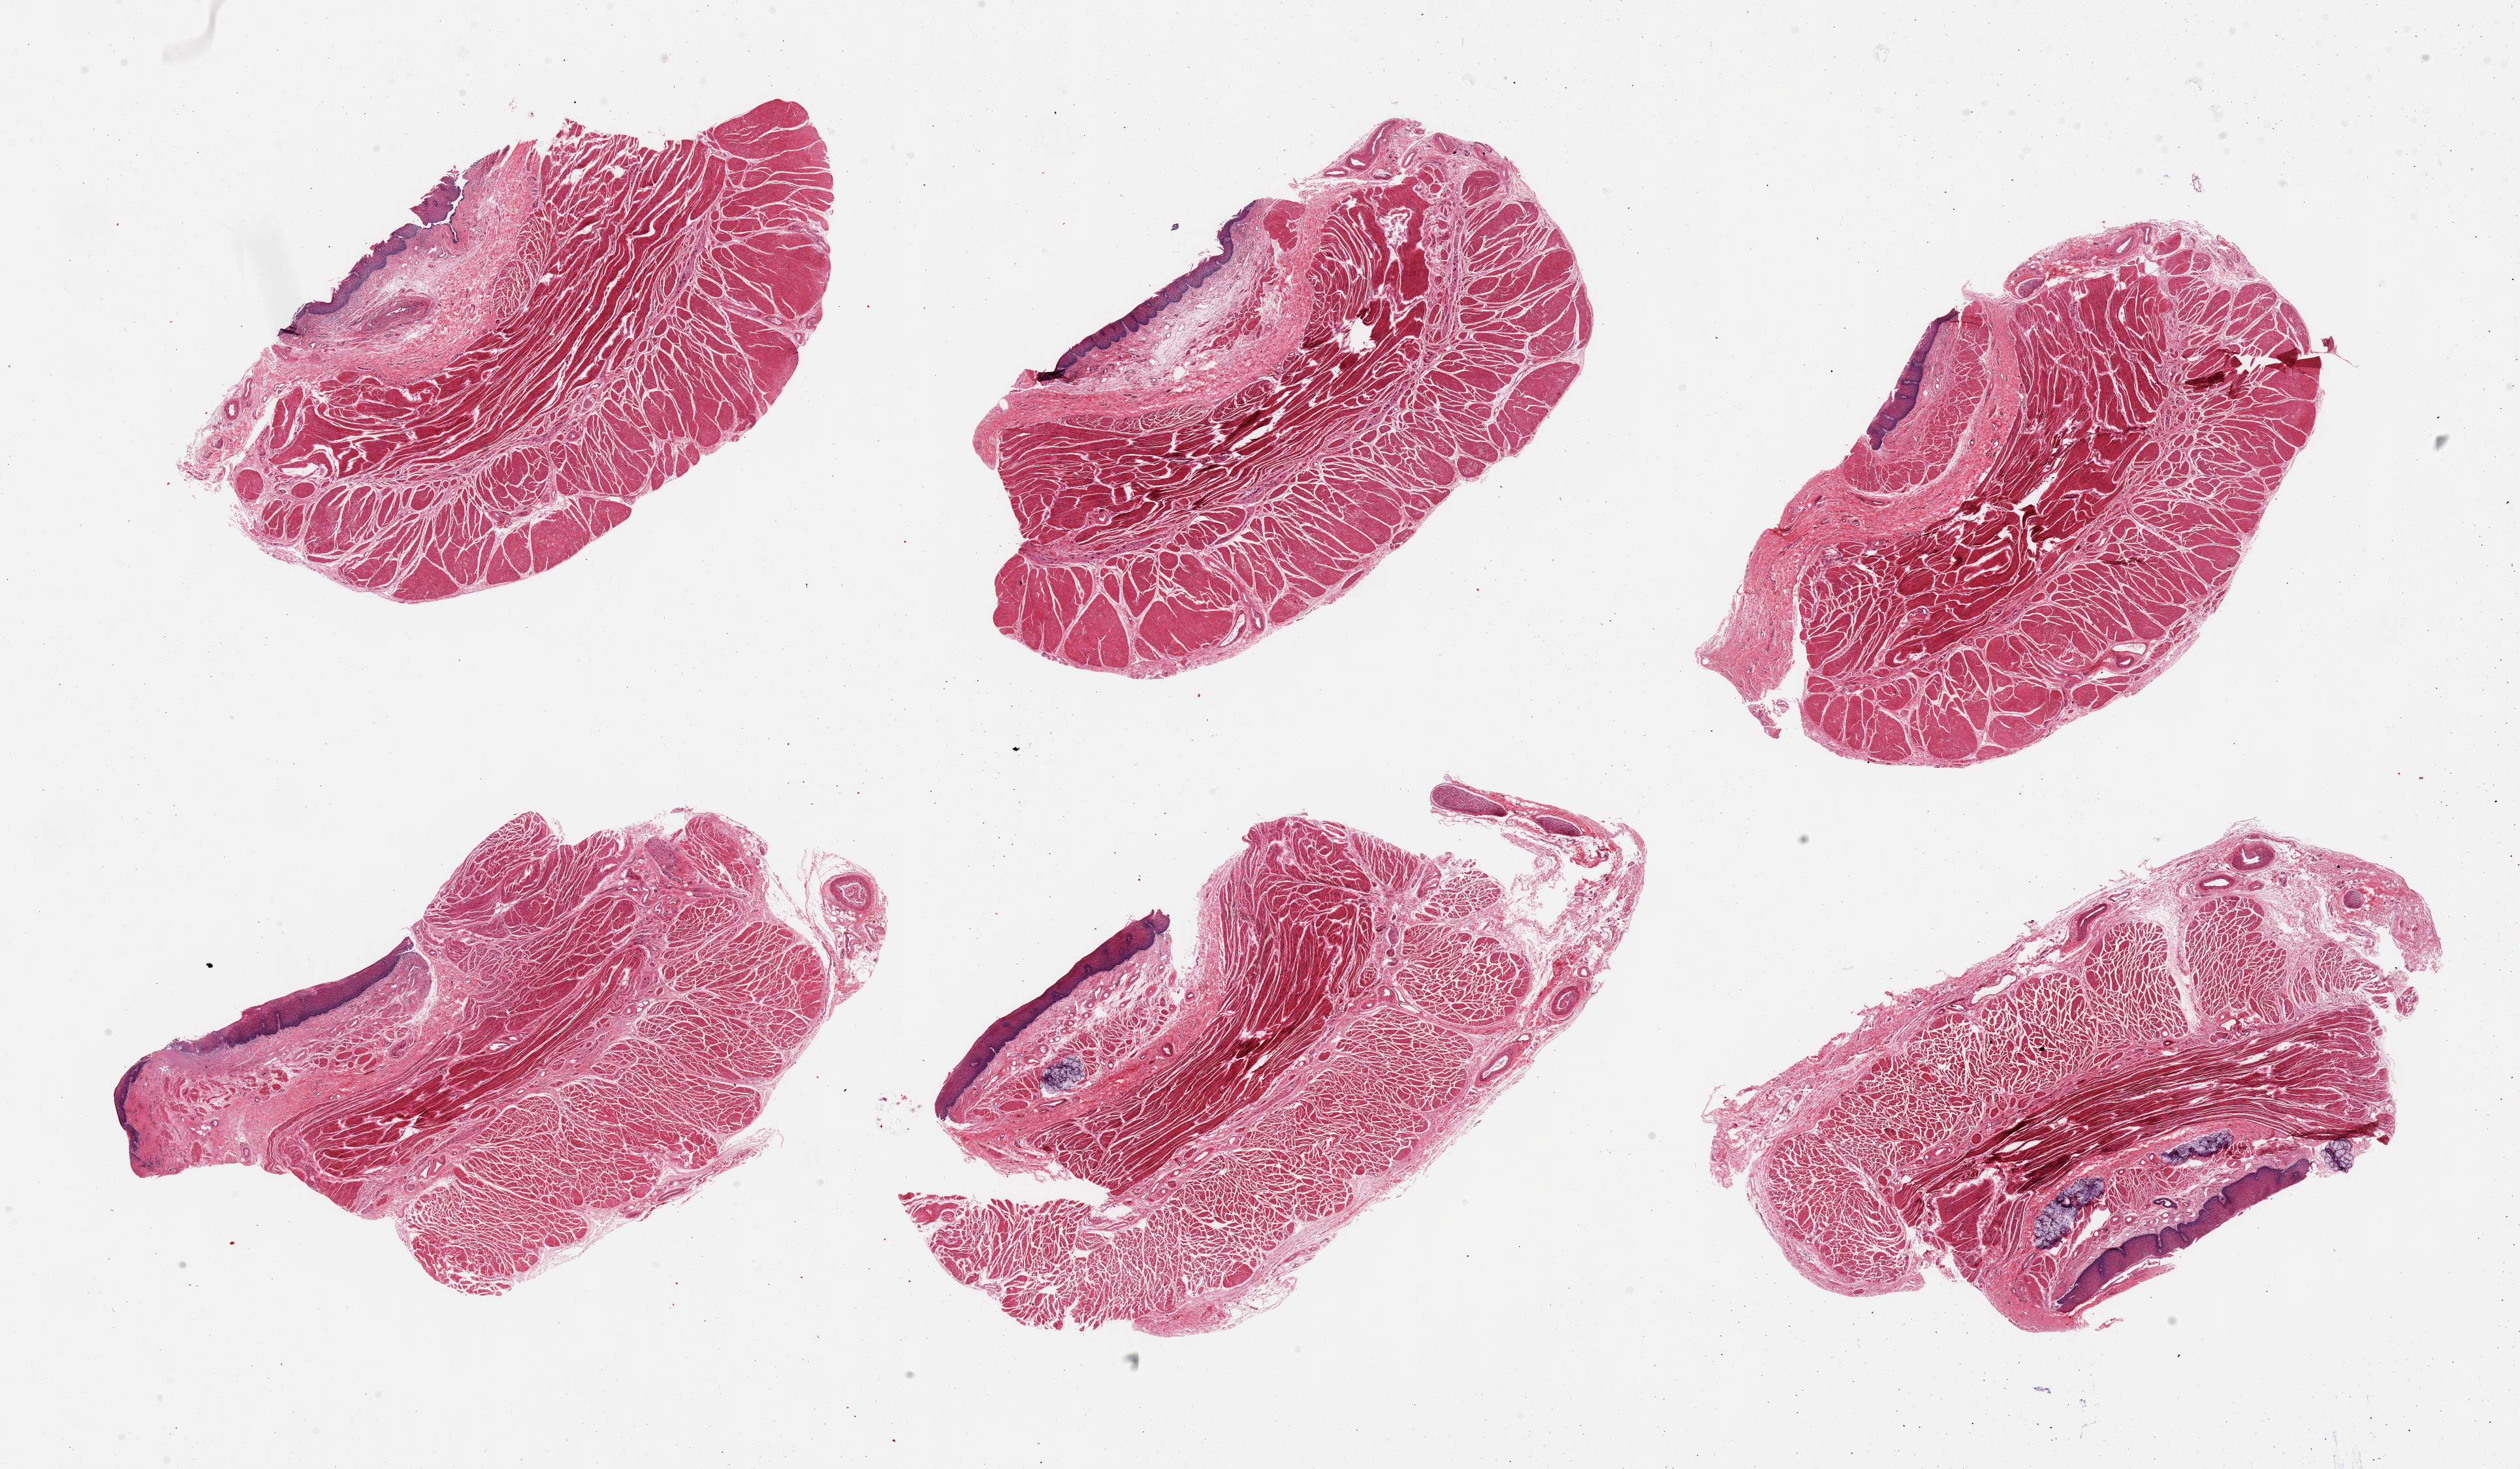
Whole-slide image, hematoxylin and eosin (H&E) stain — whole scanned area (about 30.5 x 17.8 mm) shown as a low-resolution overview; PAXgene-fixed, paraffin-embedded tissue; section of gastroesophageal junction (target tissue); tissue donor sample. Donor: female.
Pathologist's review note for this sample: 6 pieces, ~ 5% 'contaminant' squamous mucosa.